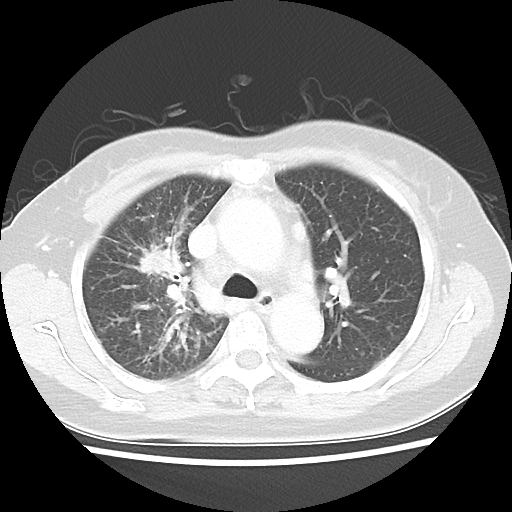
Chest CT, one axial slice; position 30 of 48 along the scan axis; lung window (W 1500 / L -600 HU); 5 mm slice thickness; 512 × 512 image matrix. Female patient, age 55 years. From the clinical record (not read from this slice): clinical TNM (as recorded): T1b N3 M1a.
Annotated regions visible in this slice (rectangle marked by the reading radiologist):
- lung tumour (recorded histology: adenocarcinoma): box from (x=138, y=244) to (x=183, y=277) px